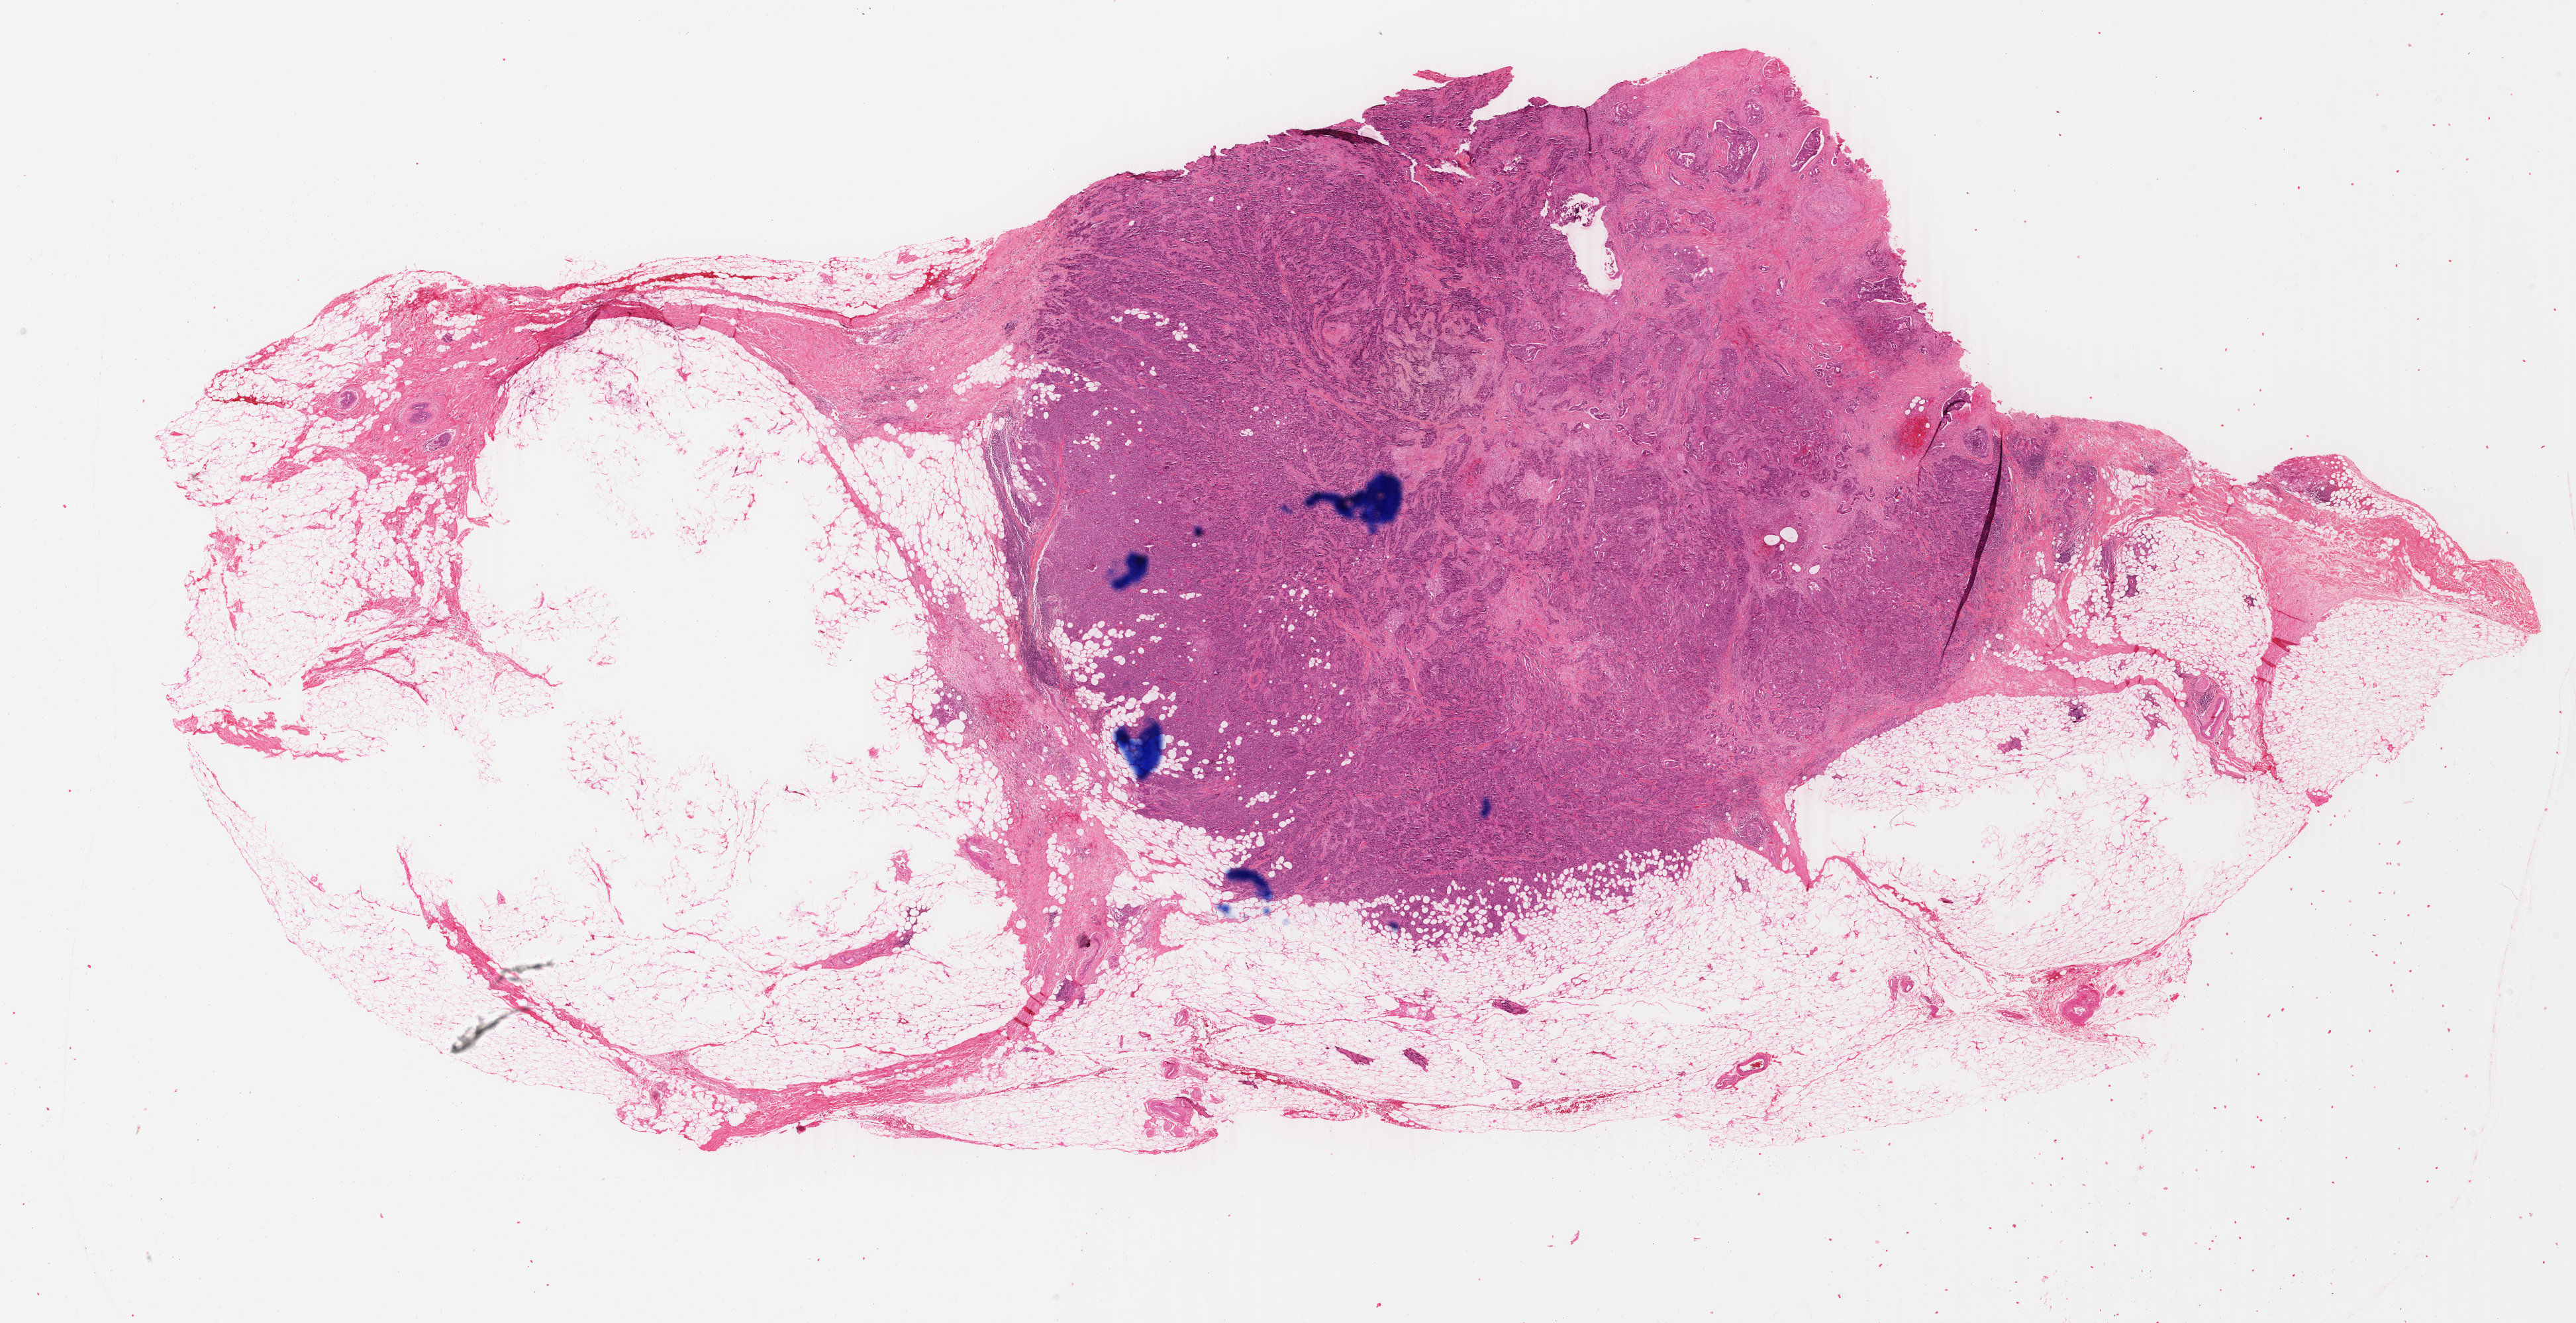
Whole-slide histology image, H&E-stained — shown as a low-resolution overview of the whole scanned area (about 30.9 x 15.9 mm), formalin-fixed paraffin-embedded (FFPE) diagnostic section, sample: primary tumour, breast. Female patient; age at initial diagnosis 61 years.
Lymph nodes positive (case pathology): 0 of 14 examined. Laterality: right. Diagnosis: Infiltrating duct carcinoma, NOS.